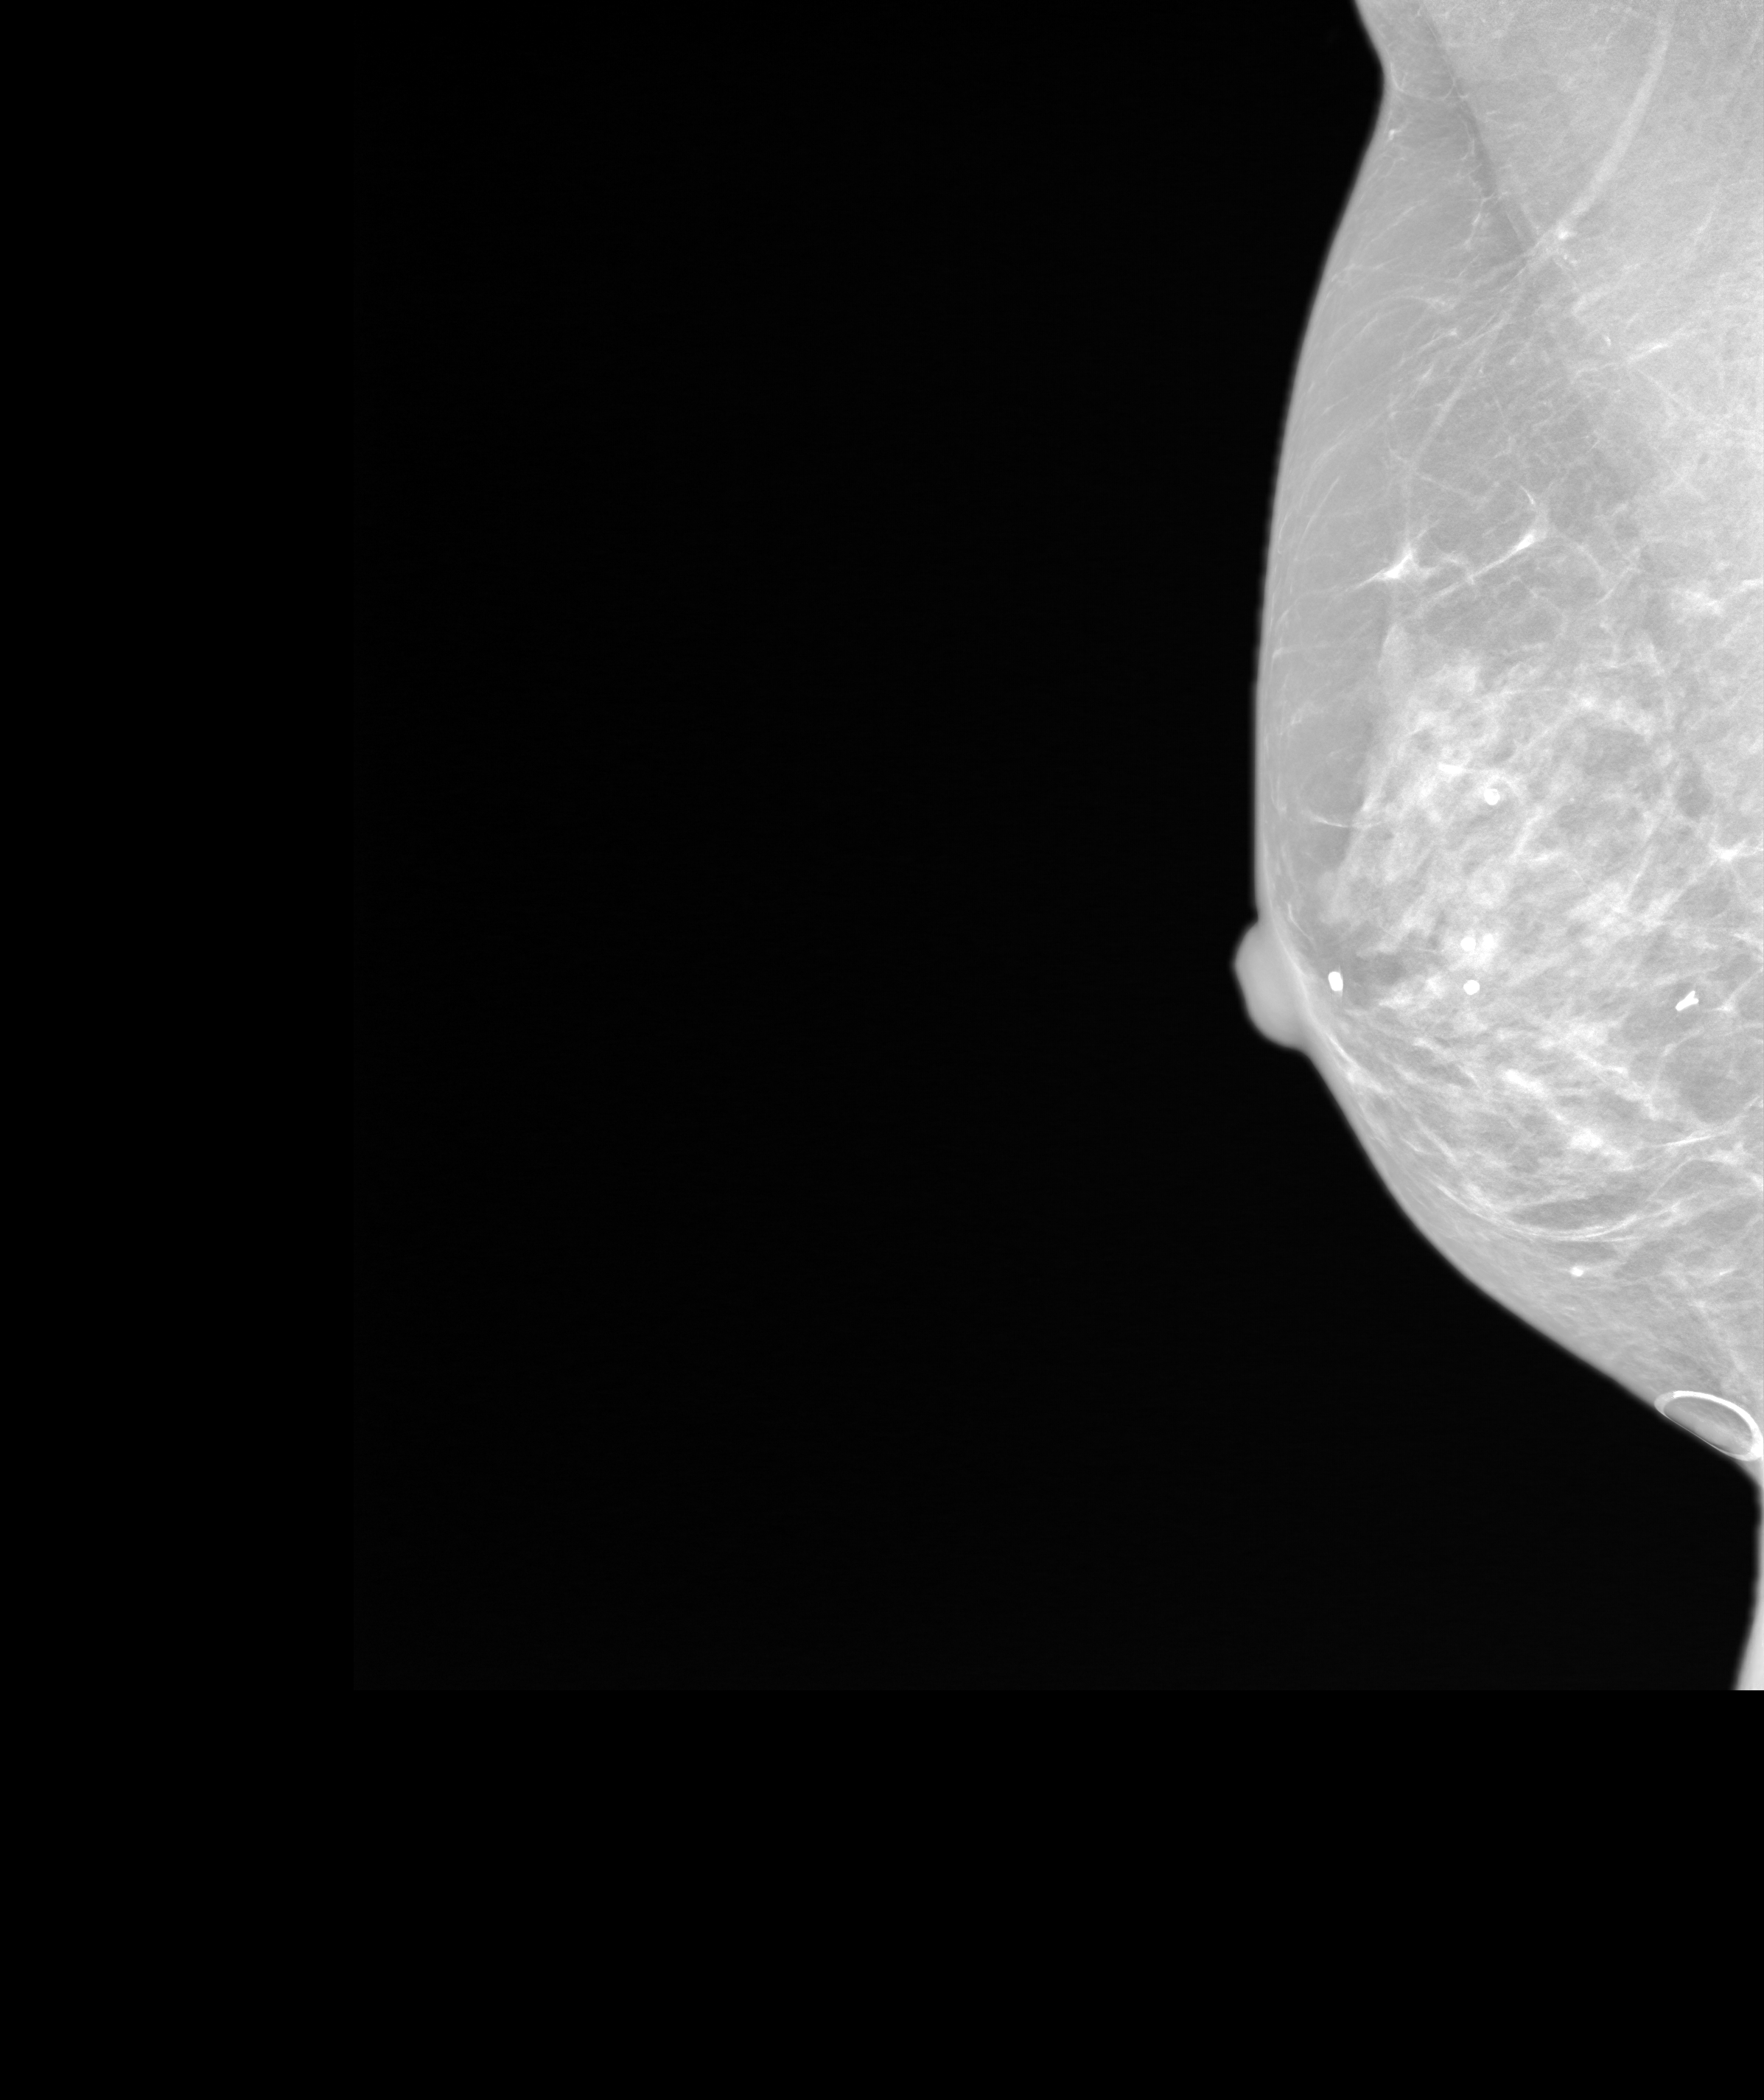
Screening examination; system: SenoIris_1SP2(440). Patient aged 65 years (female).
Image type: synthesized 2-D view from tomosynthesis. Breast: right. Projection: mediolateral oblique (MLO) view.